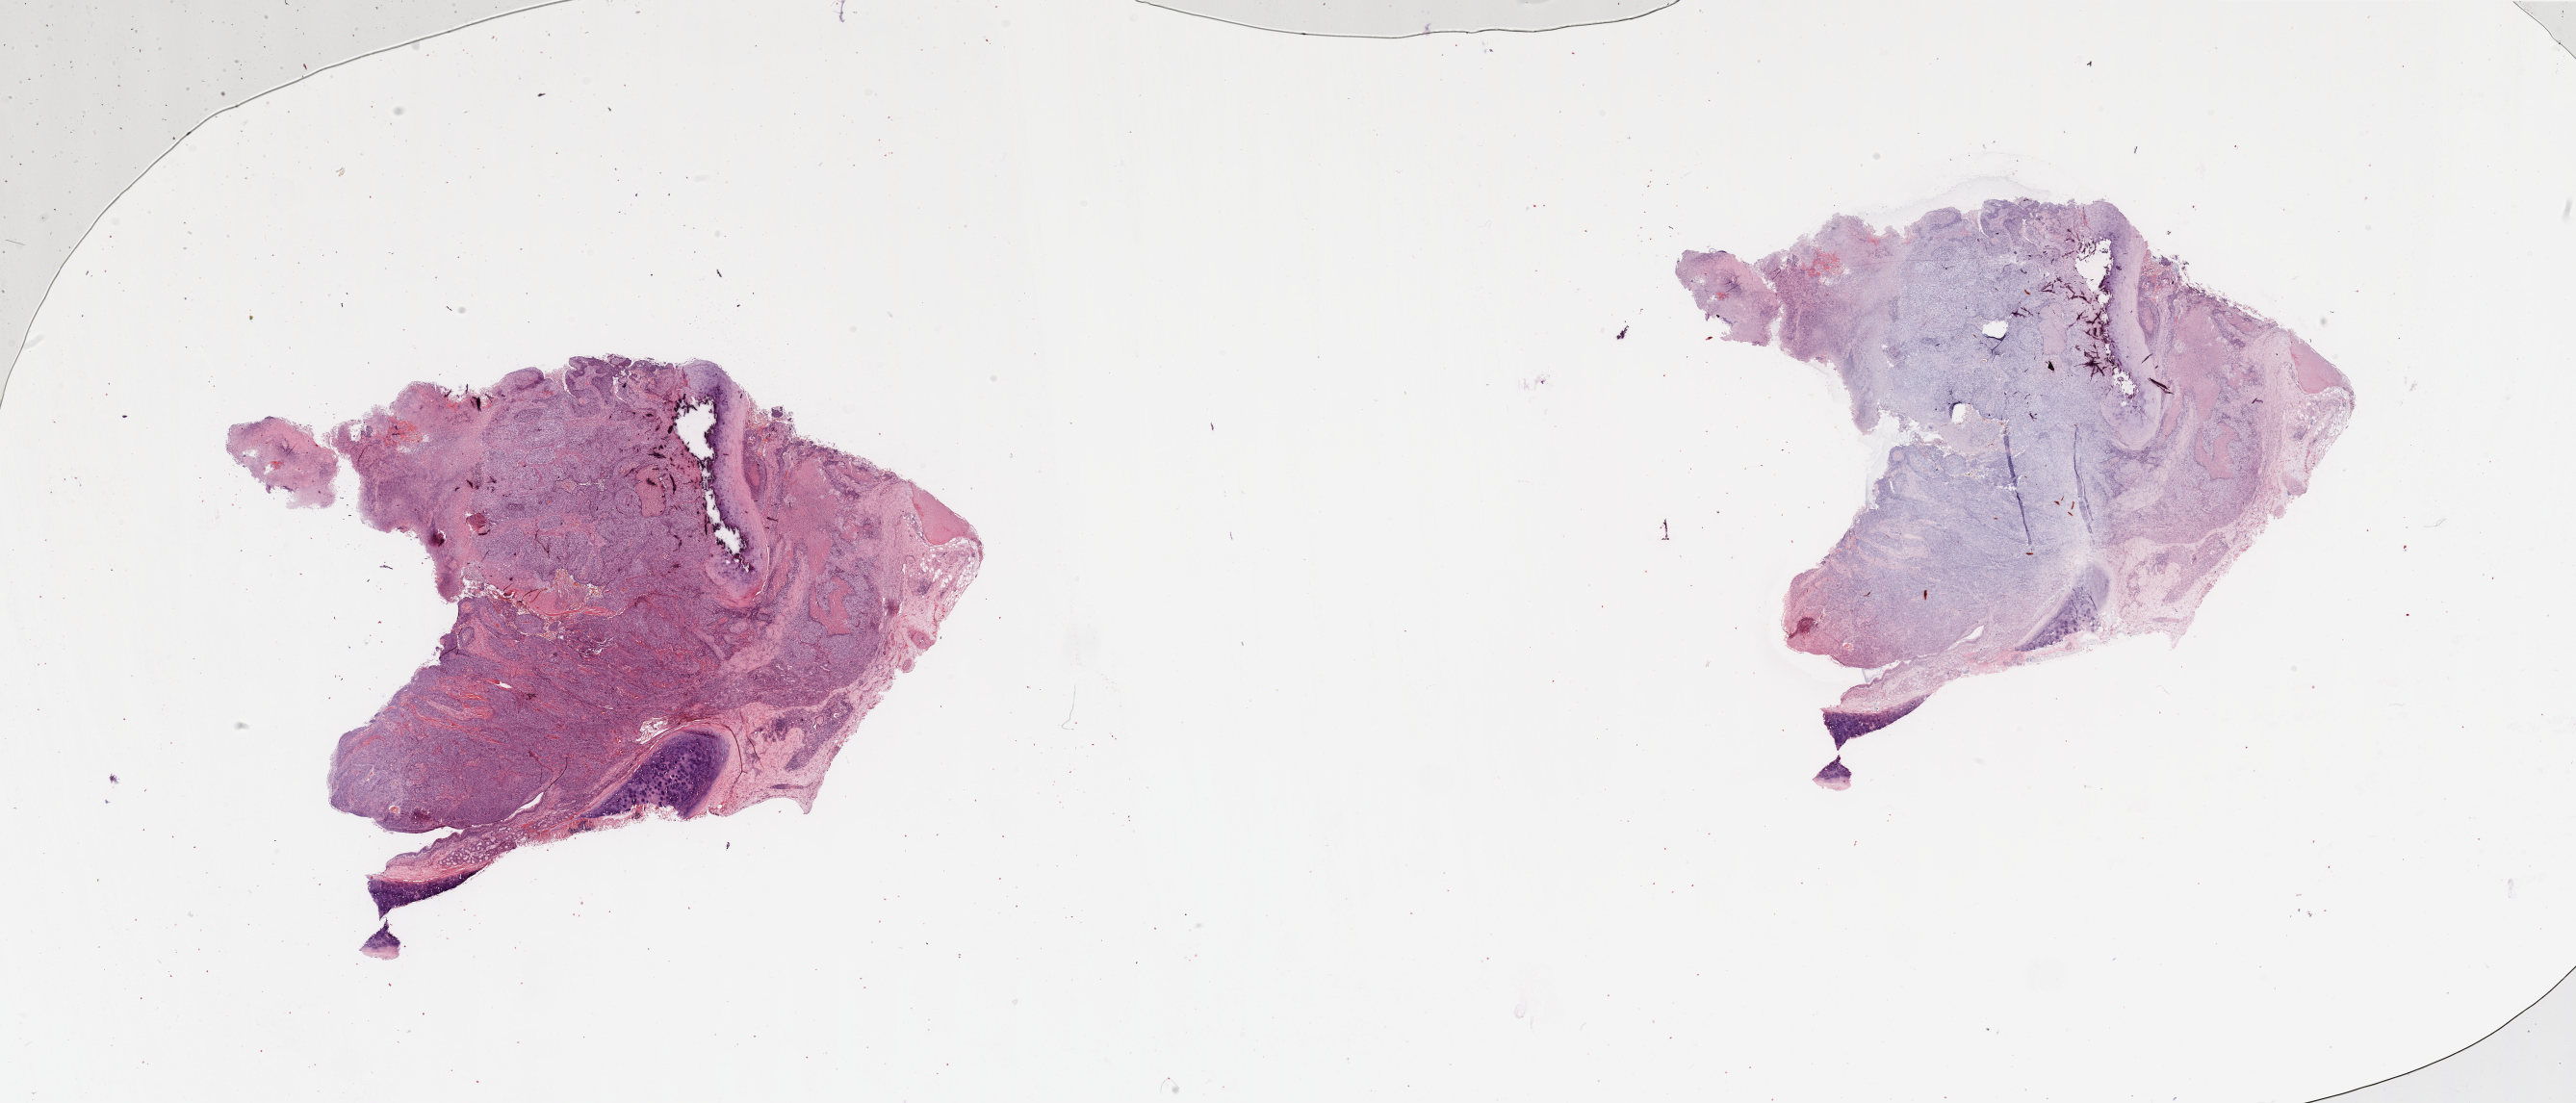
Whole-slide histology image, H&E-stained, whole scanned area (about 42.3 x 18.1 mm, acquisition: 20x scan) shown as a low-resolution overview, lung, tumour tissue. Patient: male, age 65 years. Histologic grade: G3 (poorly differentiated).
AJCC pathologic stage: IB. Histologic diagnosis: Squamous cell carcinoma, NOS.